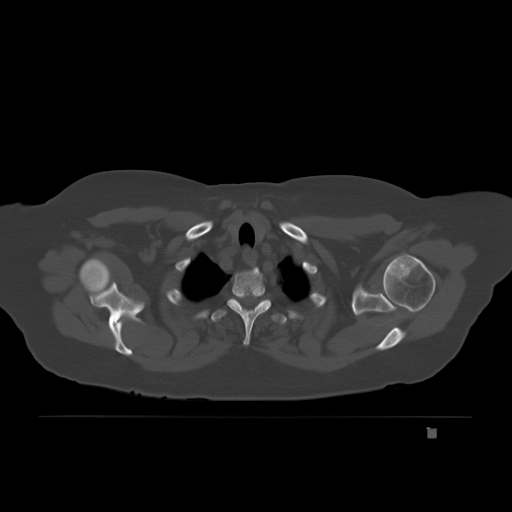
CT including the spine, one axial slice; position 171 of 221 along the scan axis; bone window (W 1800 / L 400 HU); 3 mm slice thickness; 512 × 512 image matrix, field of view 474 × 474 mm. Female patient, age 63 years. Case-level facts recorded for this patient, not image findings: primary cancer: breast.
Structures marked on this image (semi-automatically segmented with operator editing):
- T3 vertebra: bounding box (x1, y1, x2, y2) in pixels: (271, 315, 286, 321)